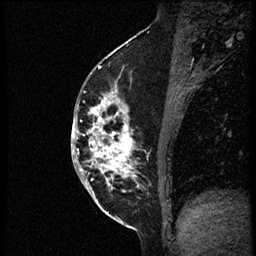
Breast MRI (dynamic contrast-enhanced), one sagittal slice; position 29 of 56 along the scan axis; dynamic contrast-enhanced study with each time point stored as its own series, time point 2 of 3 at this slice position (early post-contrast, ordered by acquisition time); 1.5 T; TE 4.2 ms, TR 21.3 ms; 2 mm slice thickness; 256 × 256 image matrix. Female patient, age 41 years. Case-level facts recorded for this patient, not image findings: setting: breast cancer imaged before/during neoadjuvant chemotherapy; receptor status: HER2-positive.
Annotated regions visible in this slice (semi-automatic segmentation, software-assisted and operator-edited):
- analysis volume of interest (the breast-tissue region the enhancement analysis was run in; not a lesion): bounding box (x1, y1, x2, y2) in pixels: (86, 73, 177, 205)
- tumour enhancement mask (voxels above the 100 % enhancement threshold inside the analysis volume of interest): (86, 76, 138, 202)